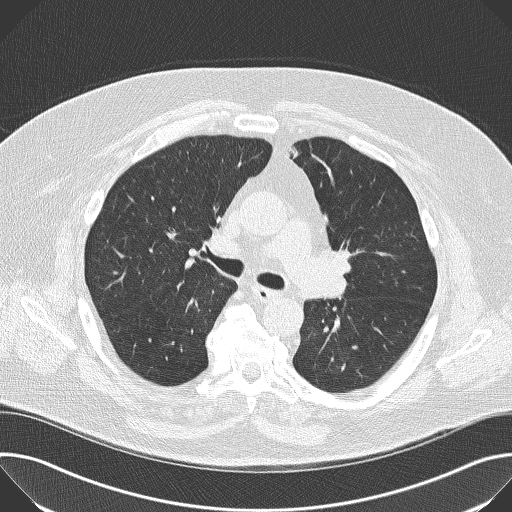
Low-dose screening chest CT, axial slice; baseline screening round; lung window (W 1500 / L -600 HU); 2 mm slice thickness; 512 × 512 image matrix. Male participant, aged 68 years at enrolment.
• Expert reader's lesion annotation, bounding box (x1, y1, x2, y2) in pixels: (318, 232, 371, 283).
• The screening reader recorded 2 non-calcified nodules or masses ≥4 mm on this exam (left lower lobe, right lower lobe); which of them this box marks is not recorded.
• Participant outcome: lung cancer diagnosed 638 days after this screen (after the second annual screen) — squamous cell carcinoma, NOS, left upper lobe, poorly differentiated (G3), stage IIB (AJCC 6th edition), 35 mm at pathology.